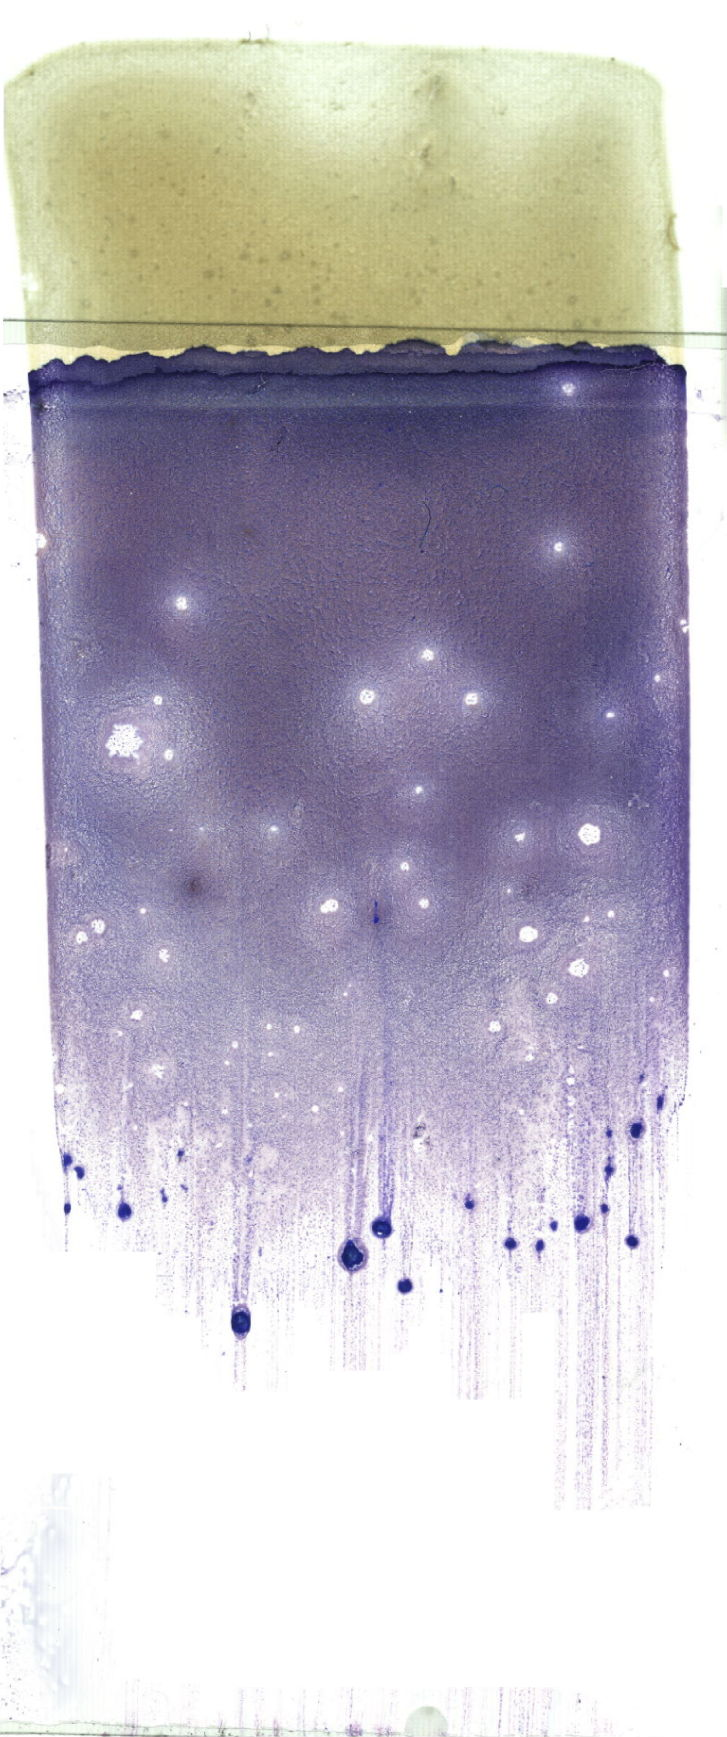
Whole-slide image of a May-Grünwald–Giemsa-stained bone marrow aspirate smear — low-resolution overview of the scanned area, about 20.6 x 49.2 mm. Female patient.
Diagnosis: Acute Megakaryoblastic Leukemia.